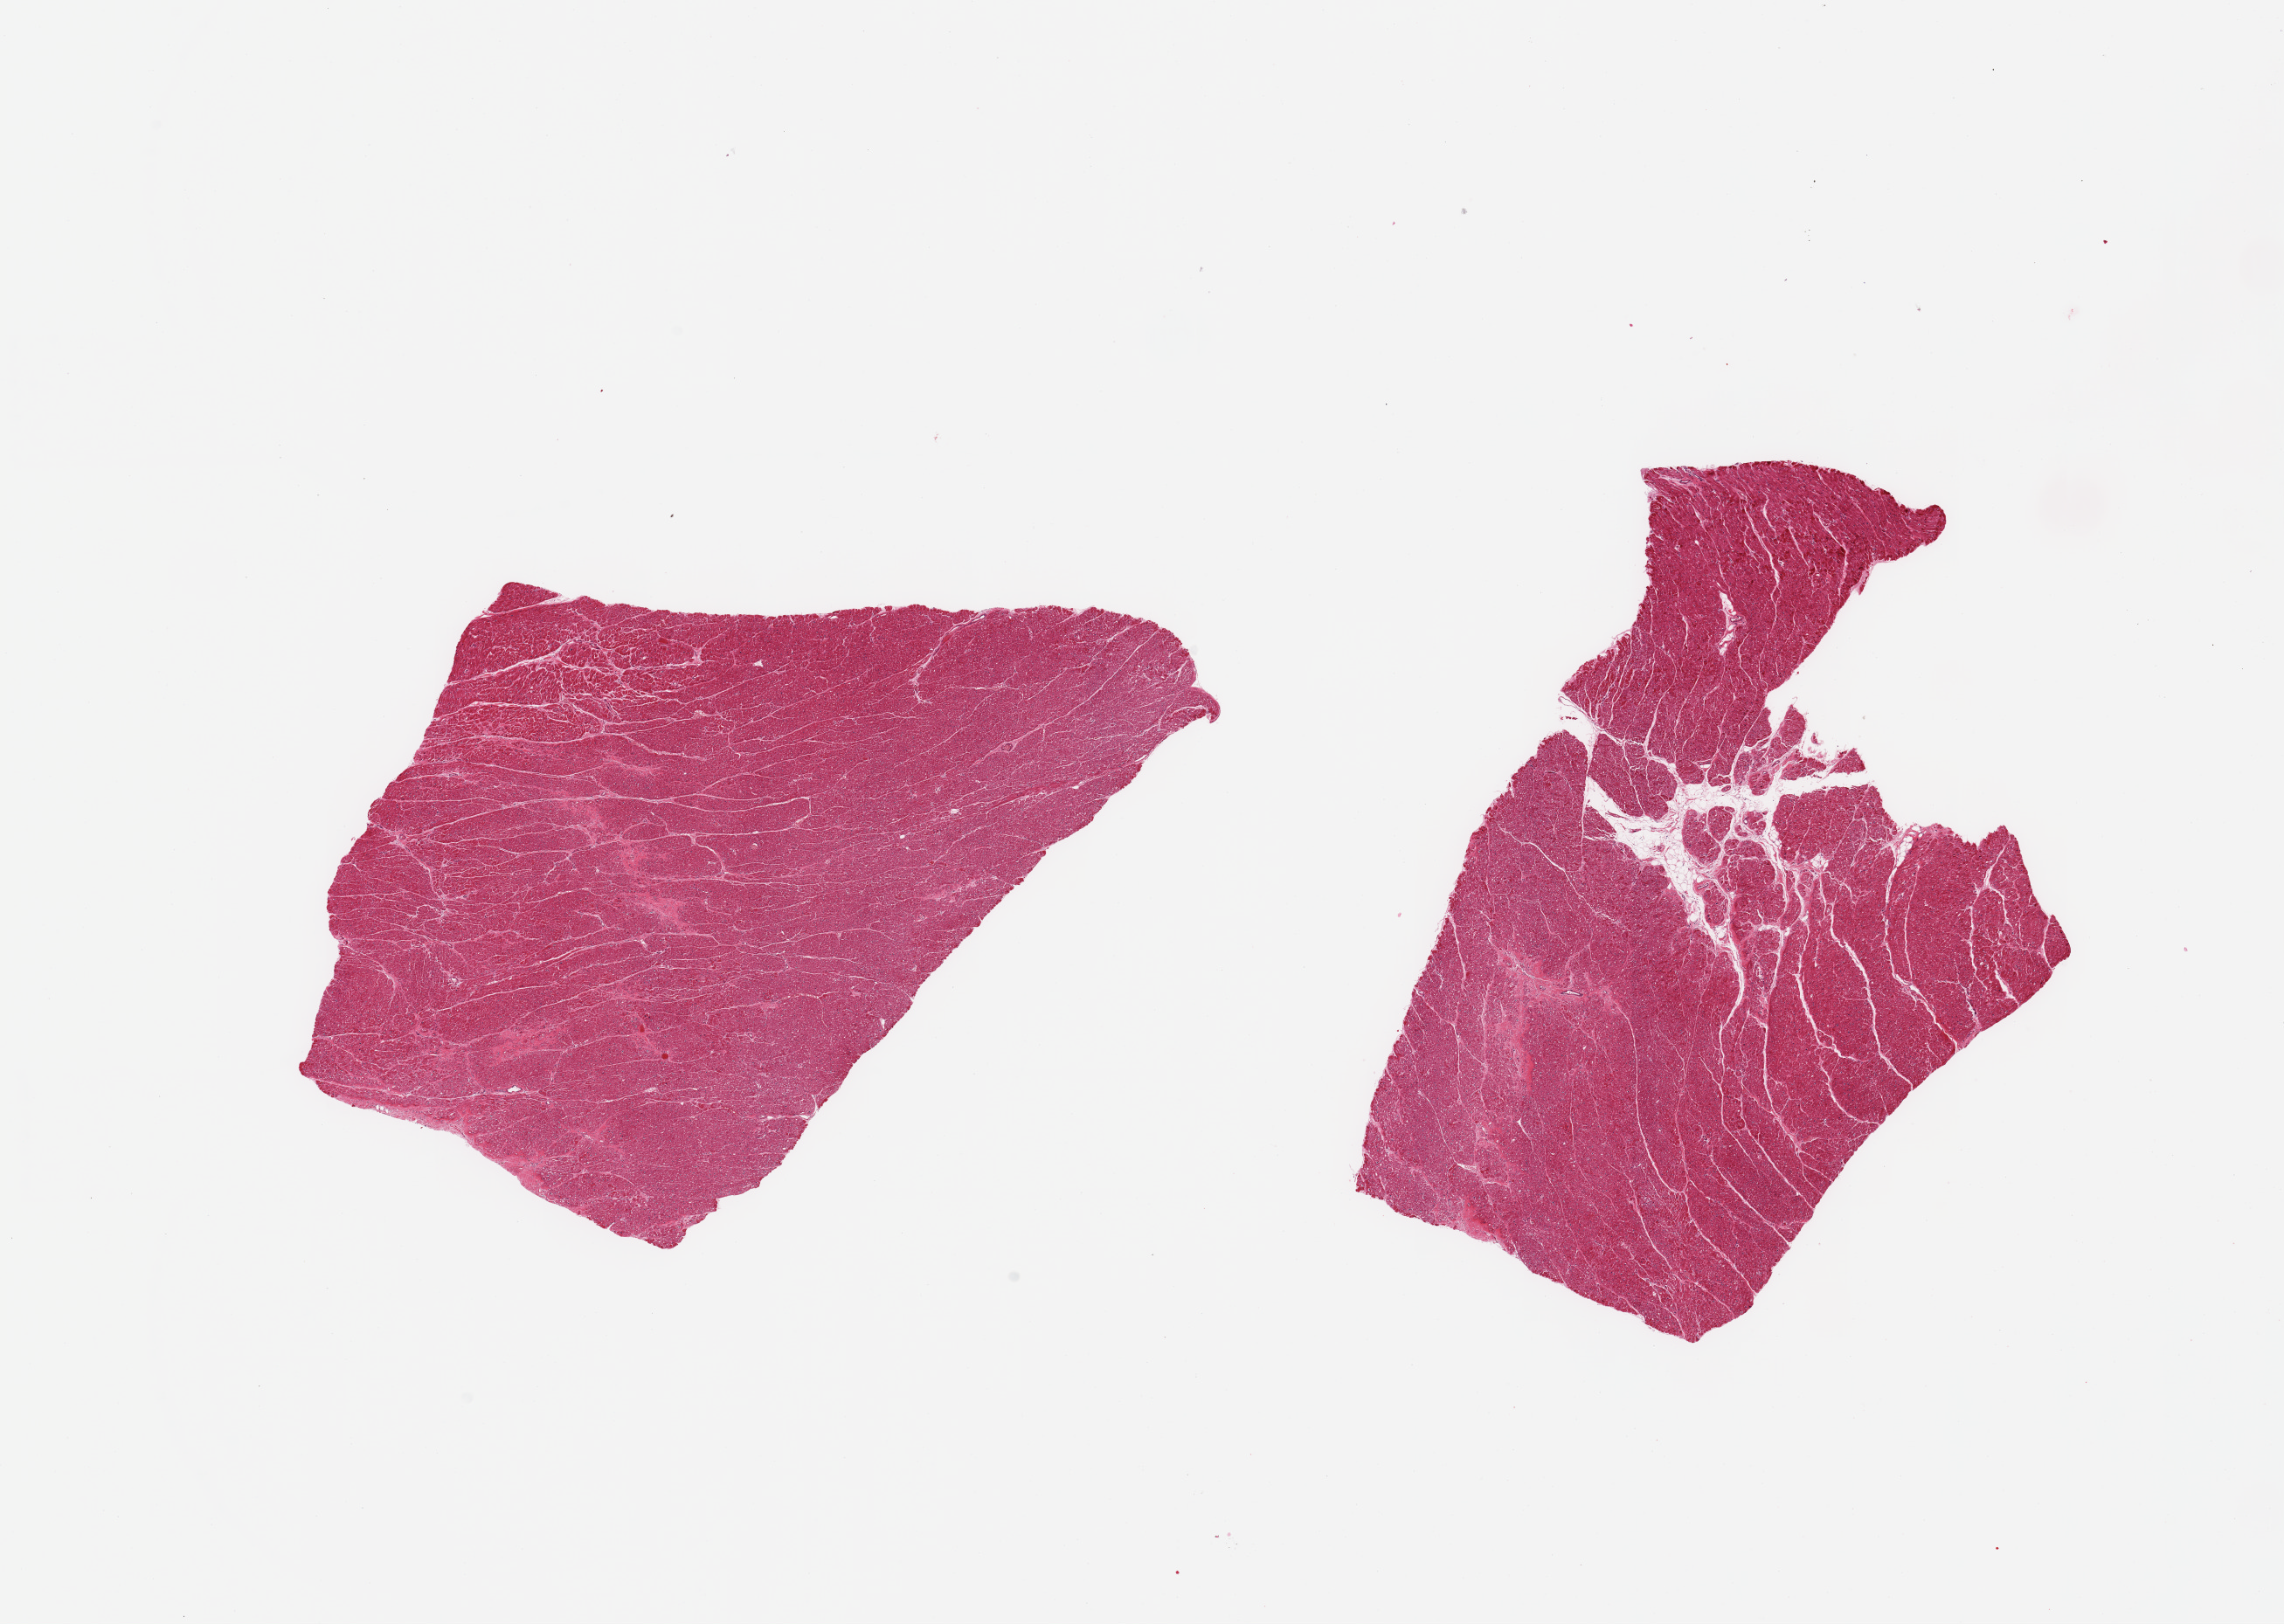
Hematoxylin and eosin (H&E) whole-slide image — low-resolution overview of the scanned area, about 20.7 x 14.7 mm; PAXgene-fixed, paraffin-embedded tissue; section of heart (target tissue); tissue donor sample.
- review note (as recorded): 2 pieces, patchy remote microinfarcts